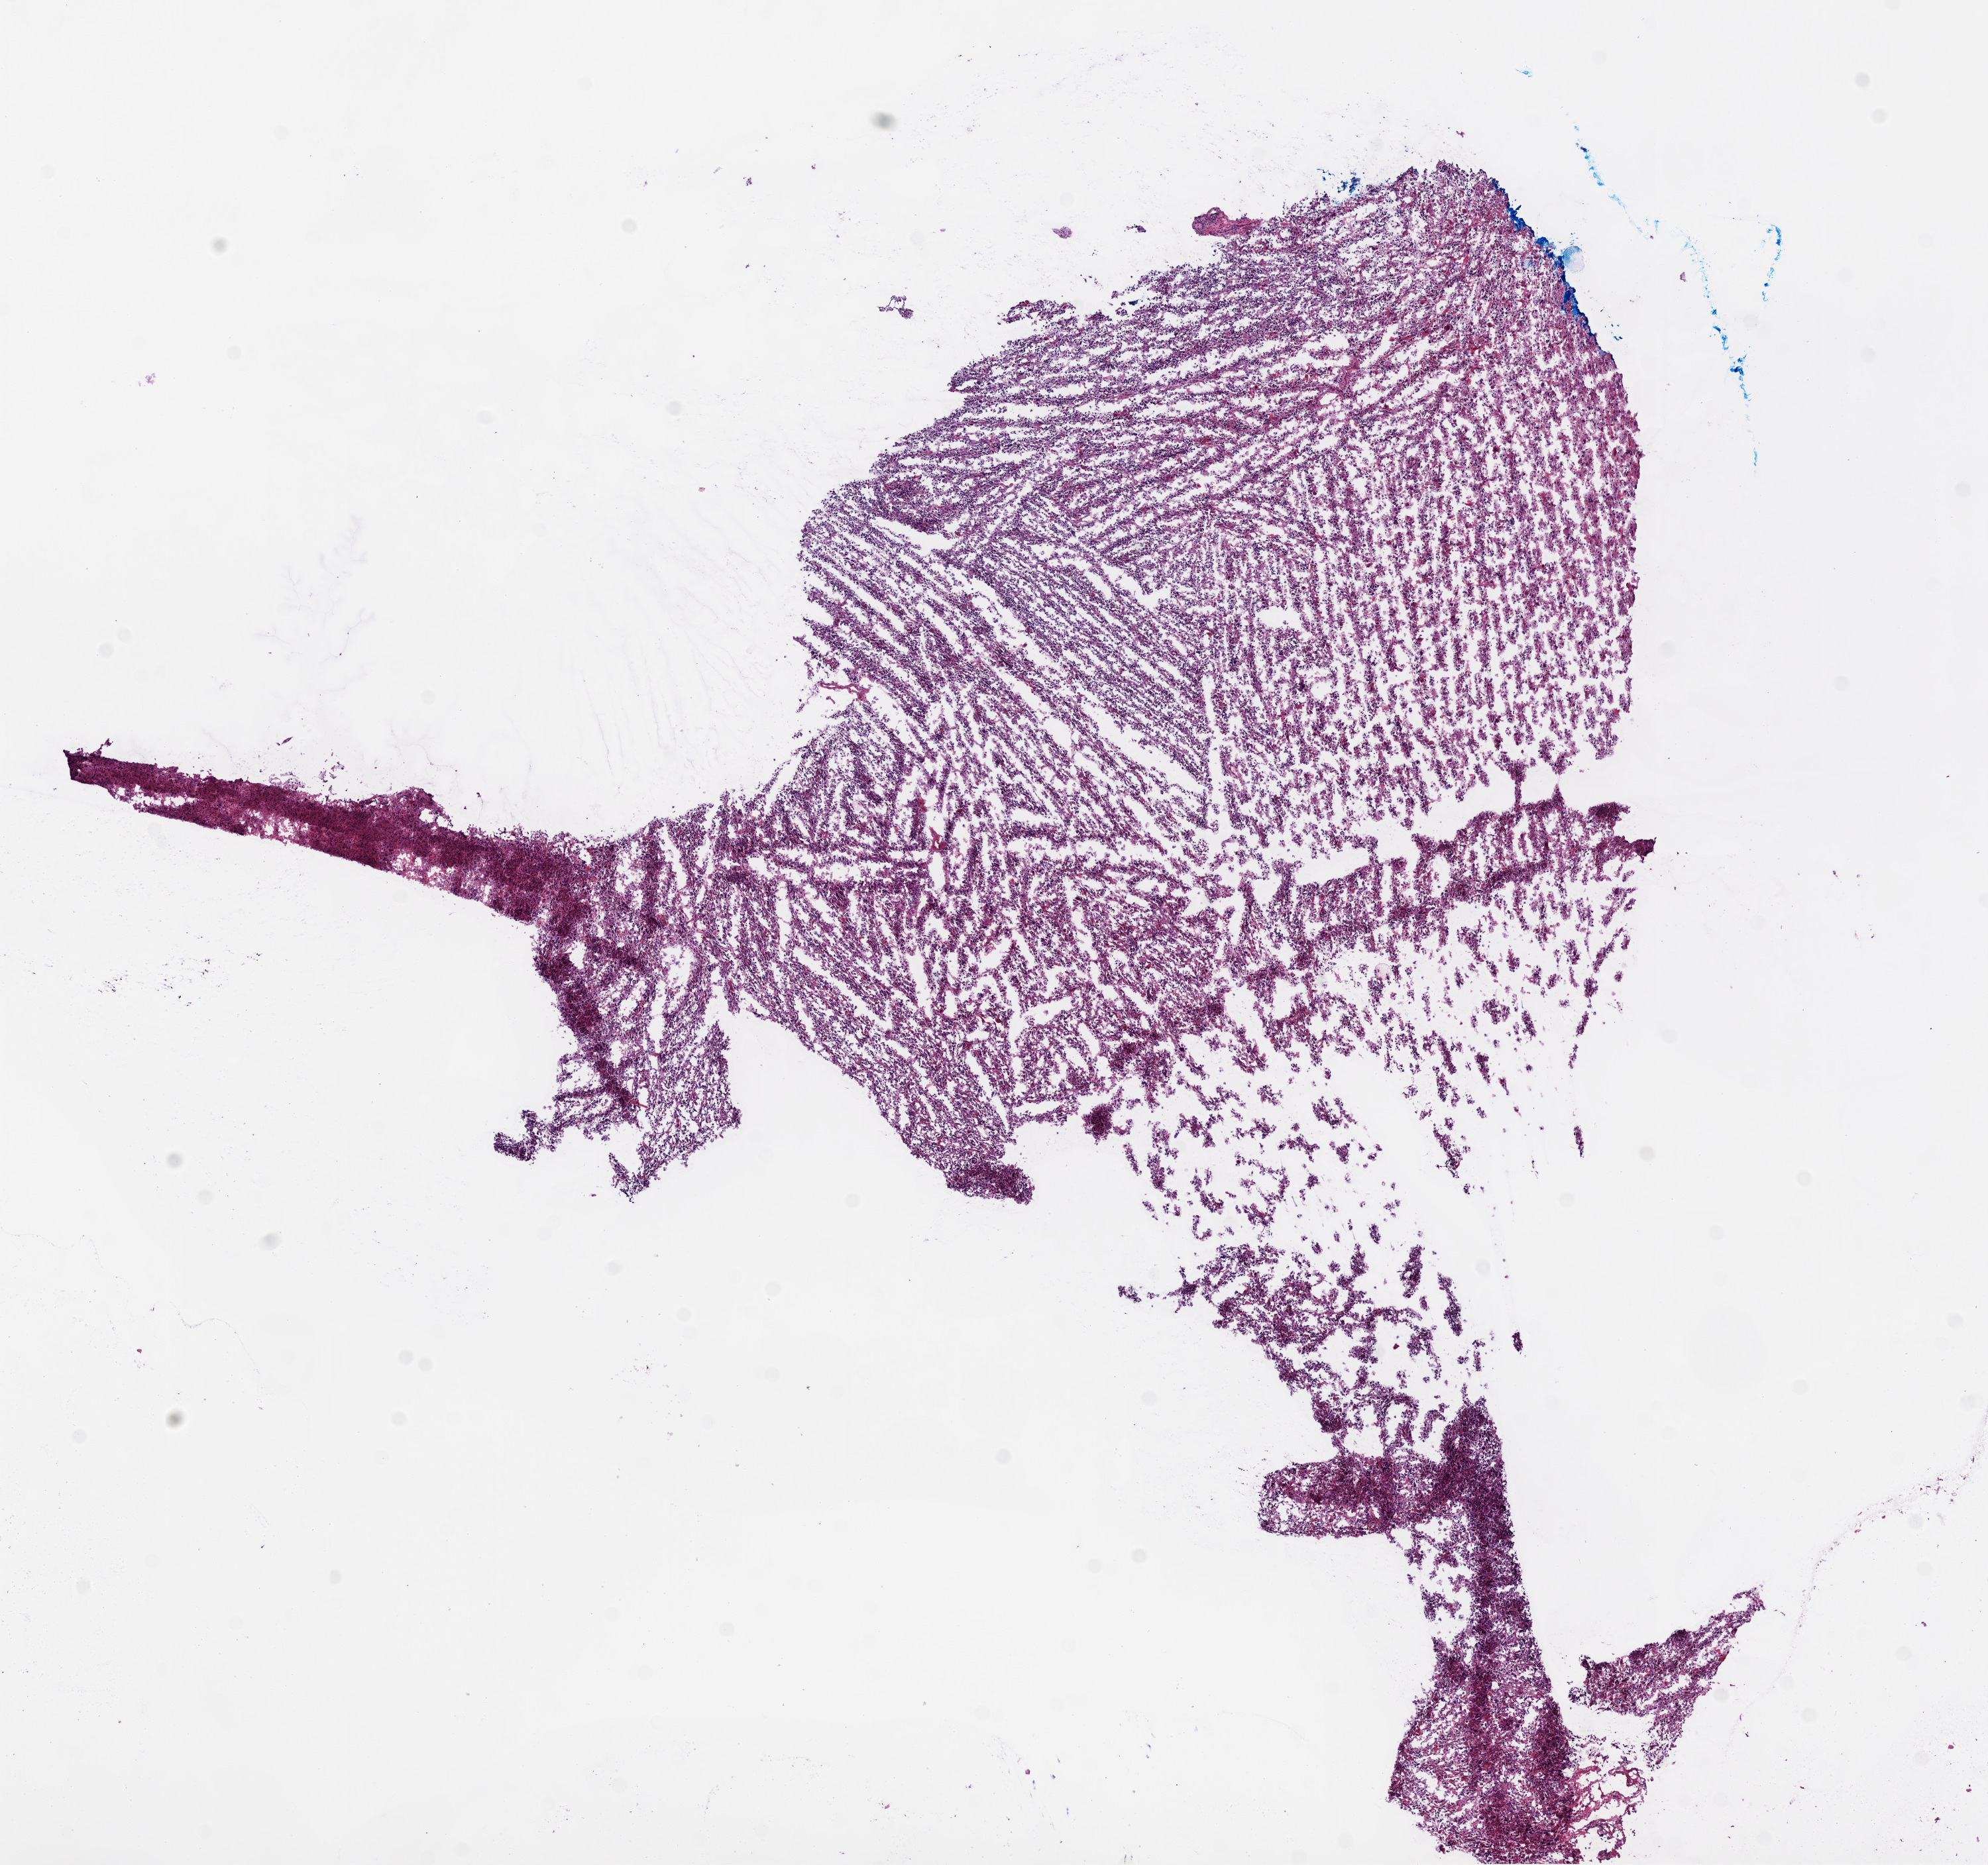
H&E-stained whole-slide image, a low-resolution overview of the entire scanned area, about 12.0 x 11.3 mm (acquisition: 20x scan), frozen section from the bottom of the tissue portion, primary tumour sample from the brain. Male, age 60 years at initial diagnosis. Pathologist review of this section (percent, as recorded): tumour cells 100%, tumour nuclei 85%, normal cells 0%, stromal cells 0%, necrosis 0%.
Pathologic diagnosis: Glioblastoma.